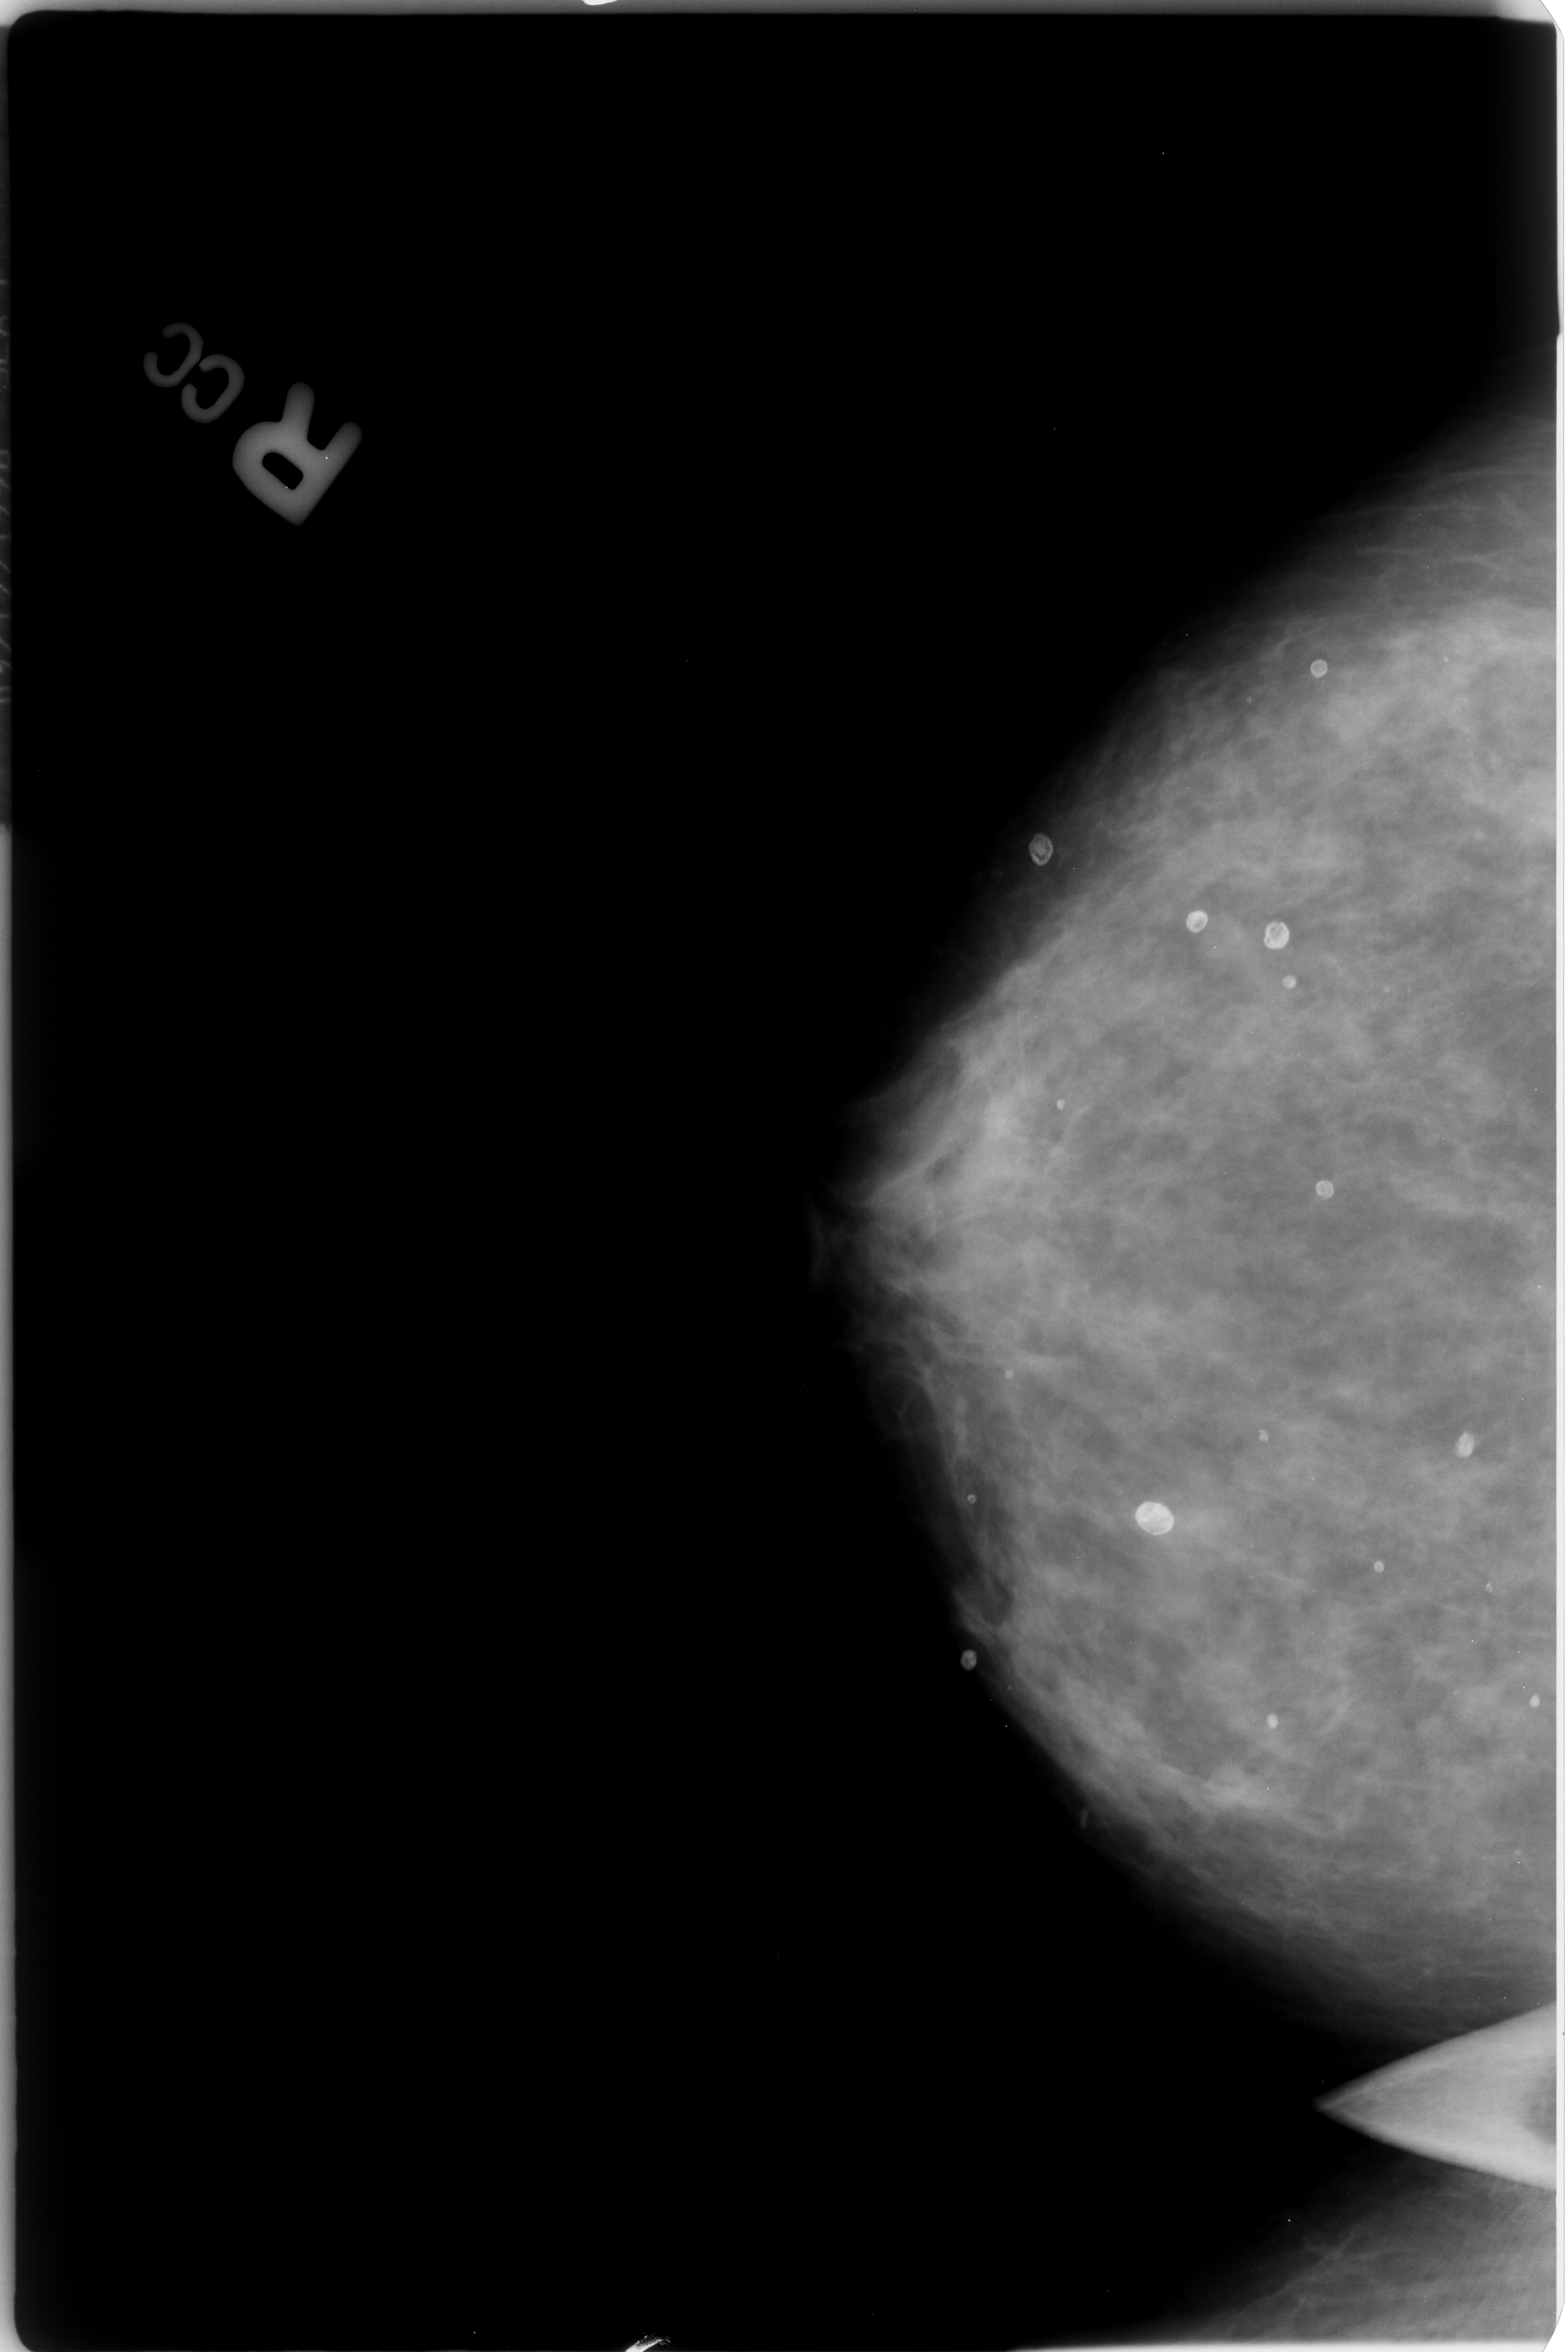
Scanned film-screen mammogram. Right breast. Craniocaudal (CC) view. BI-RADS breast density category 3 (scale 1–4). 1568 × 2352 image matrix.
Expert-marked regions of interest on this image (one box per marked abnormality):
- Finding 1 of 6: calcifications, morphology round and regular / eggshell; BI-RADS assessment category 2; subtlety rating 3 on a 1 (subtle) to 5 (obvious) scale; outcome (as recorded, no biopsy): benign without callback (not worked up further): bounding box (x1, y1, x2, y2) in pixels: (1122, 1470, 1197, 1573)
- Finding 2 of 6: calcifications, morphology round and regular / eggshell; BI-RADS assessment category 2; outcome (as recorded, no biopsy): benign without callback (not worked up further): (1167, 886, 1246, 952)
- Finding 3 of 6: calcifications, morphology round and regular / eggshell; BI-RADS assessment category 2; outcome (as recorded, no biopsy): benign without callback (not worked up further): (1237, 902, 1316, 948)
- Finding 4 of 6: calcifications, morphology round and regular / eggshell; BI-RADS assessment category 2; subtlety rating 3 on a 1 (subtle) to 5 (obvious) scale; outcome (as recorded, no biopsy): benign without callback (not worked up further): (1282, 1155, 1361, 1218)
- Finding 5 of 6: calcifications, morphology round and regular / eggshell; BI-RADS assessment category 2; subtlety rating 3 on a 1 (subtle) to 5 (obvious) scale; benign; no additional work-up was recommended (outcome (as recorded, no biopsy): benign without callback): (1286, 649, 1353, 712)
- Finding 6 of 6: calcifications, morphology round and regular / eggshell; BI-RADS assessment category 2; outcome (as recorded, no biopsy): benign without callback (not worked up further): (1437, 1404, 1496, 1471)